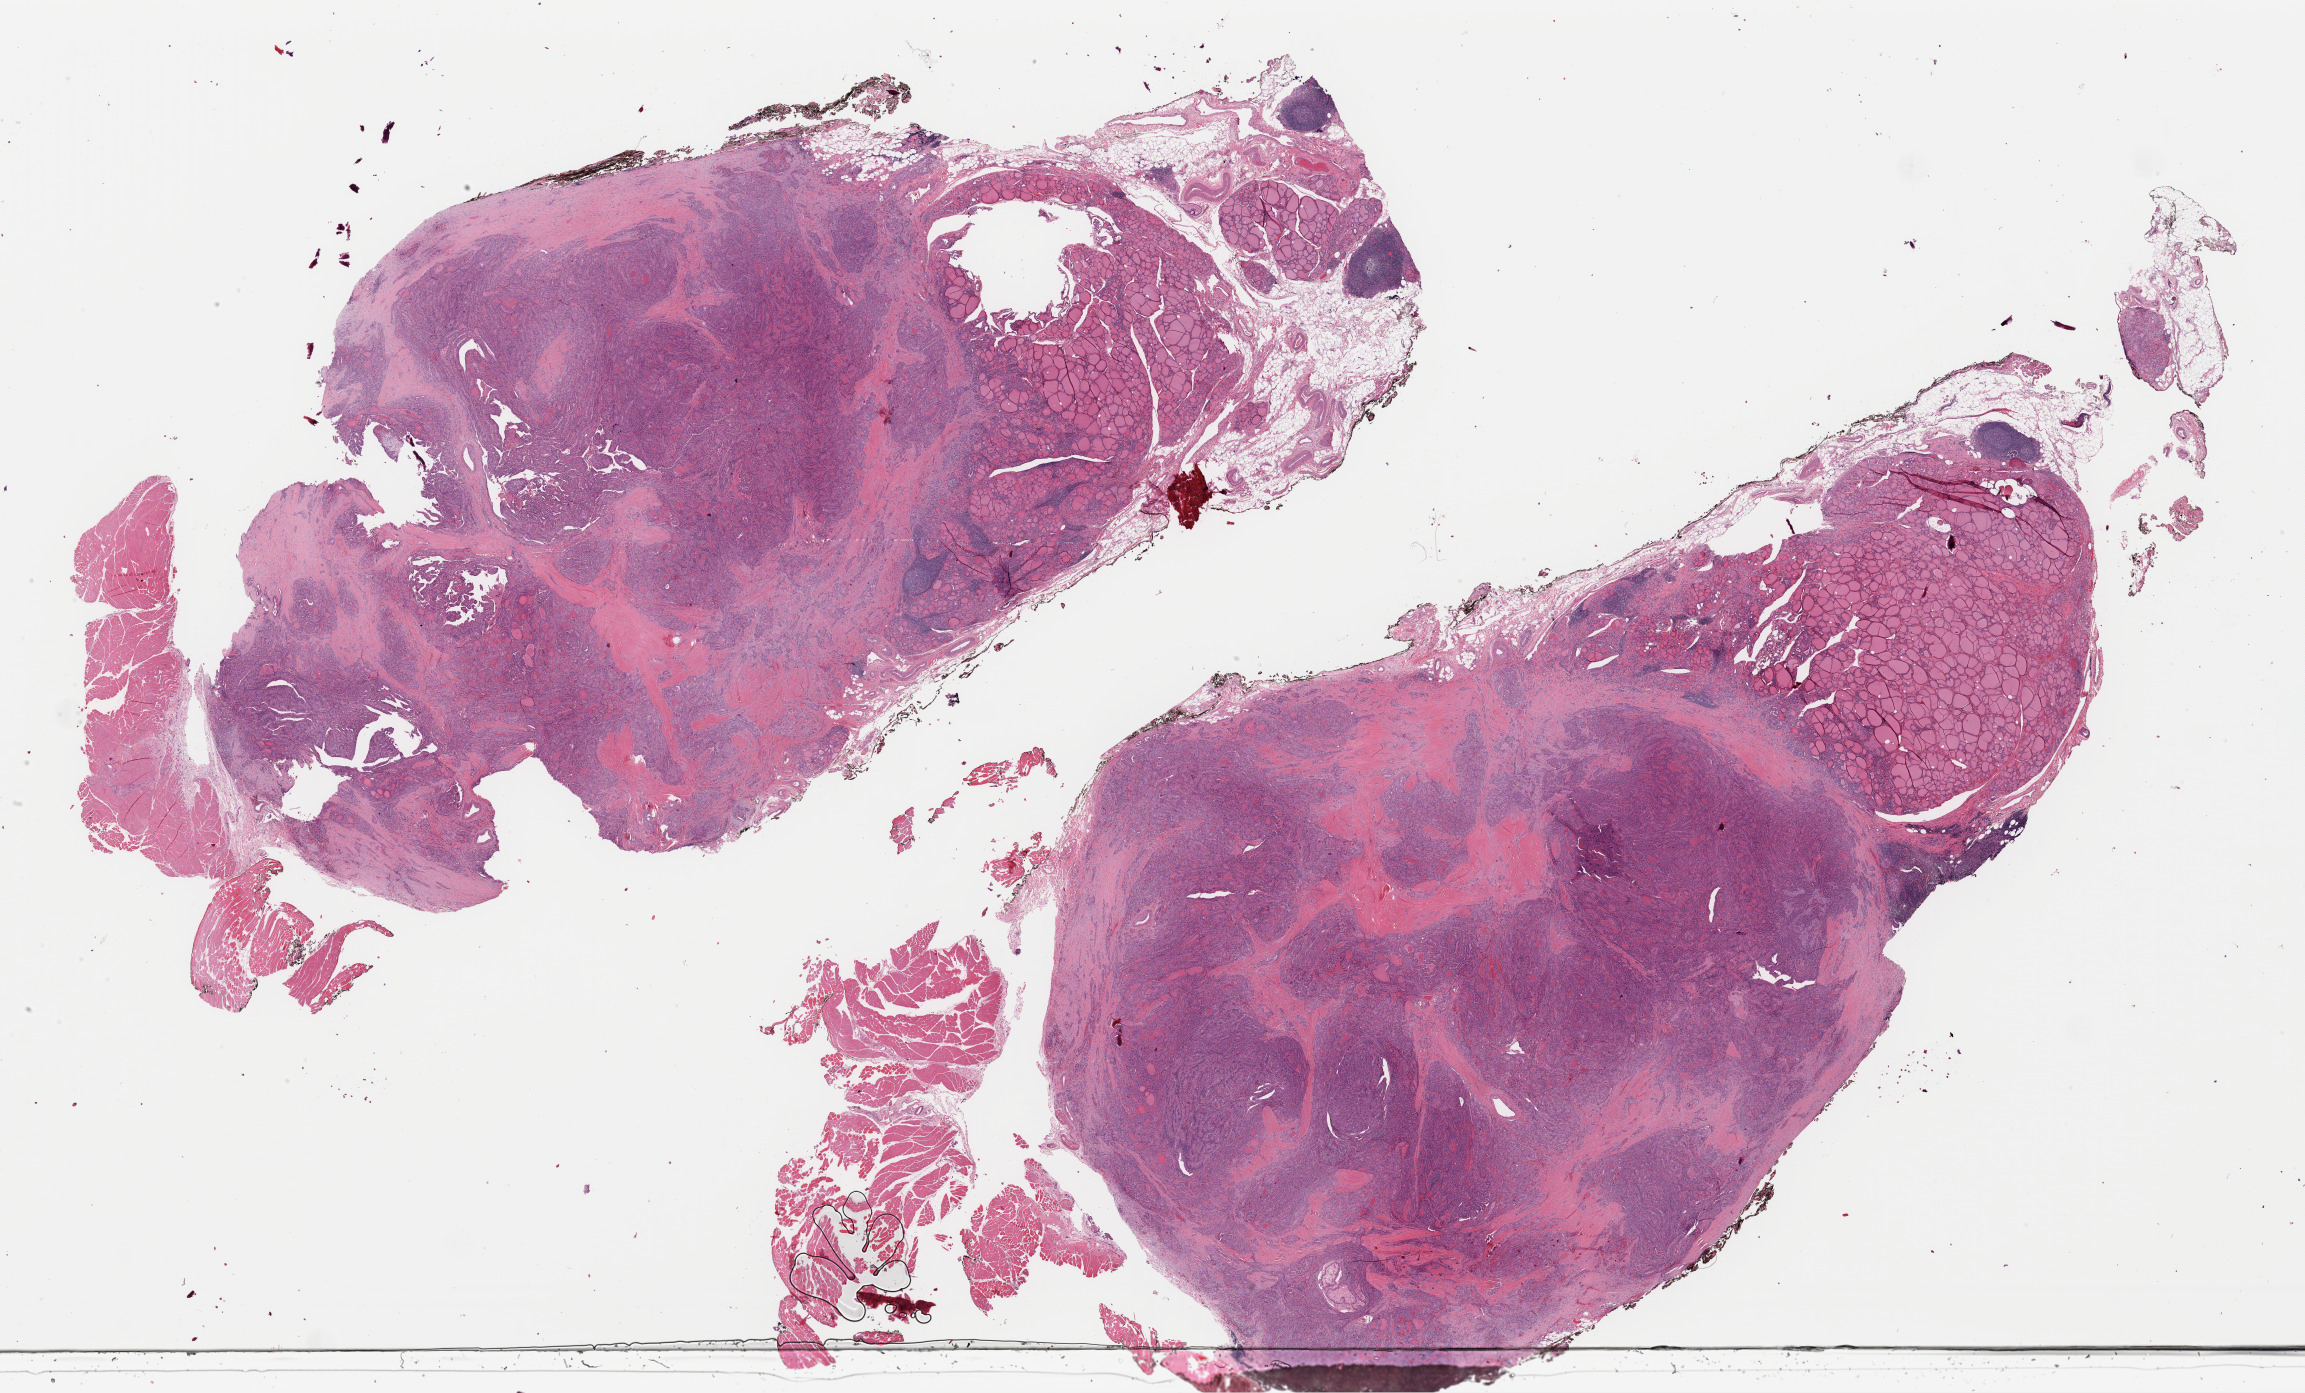
Digitized H&E-stained tissue section (whole slide), low-resolution overview of the scanned area, about 36.4 x 22.0 mm; formalin-fixed paraffin-embedded (FFPE) diagnostic section; primary tumour sample from the thyroid. Female, age 51 years at initial diagnosis.
Lymph nodes positive (case pathology): 0 of 6 examined. Laterality: bilateral. AJCC pathologic stage: III (7th edition). Histologic diagnosis: Papillary carcinoma, columnar cell (thyroid gland).